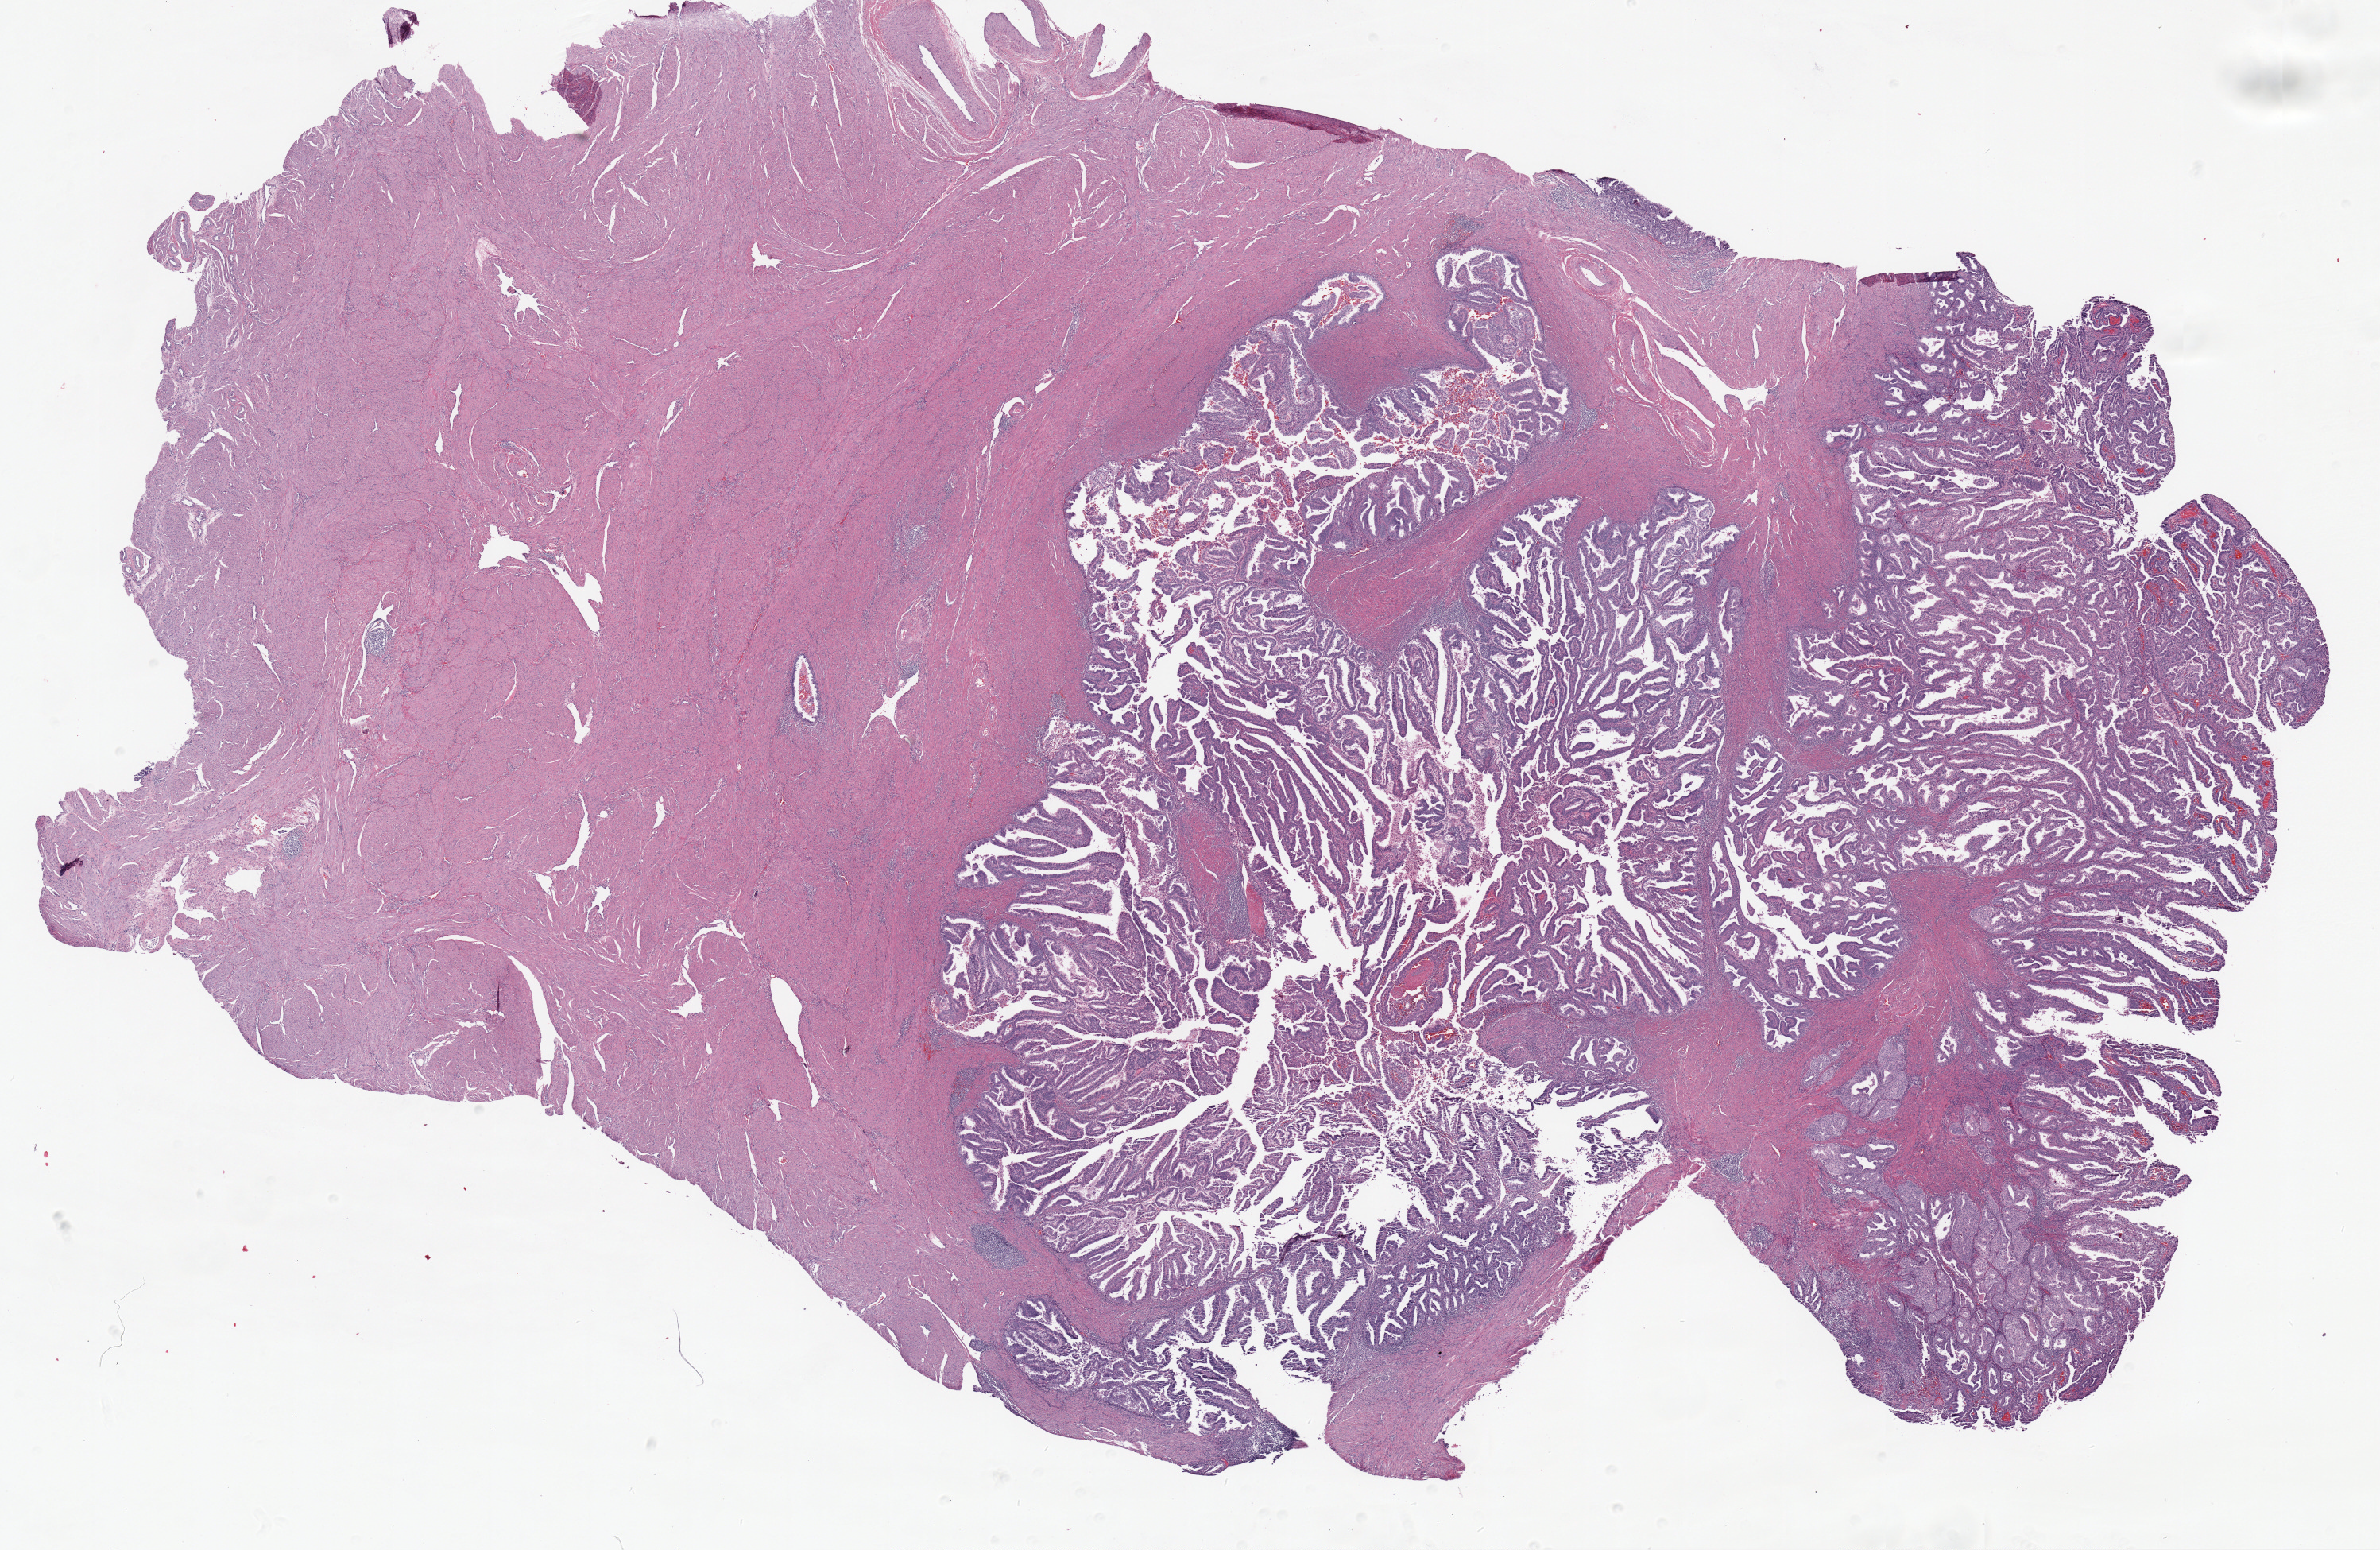
Whole-slide histology image, Hematoxylin and eosin (H&E) stained, a low-resolution overview of the entire scanned area, about 23.9 x 15.5 mm (acquisition: 20x scan), FFPE section, primary tumour sample from the uterus. Female patient; age at initial diagnosis 33 years. Histologic grade: G3 (poorly differentiated).
Diagnosis: Endometrioid adenocarcinoma, NOS (endometrium). FIGO stage: IIIC2.